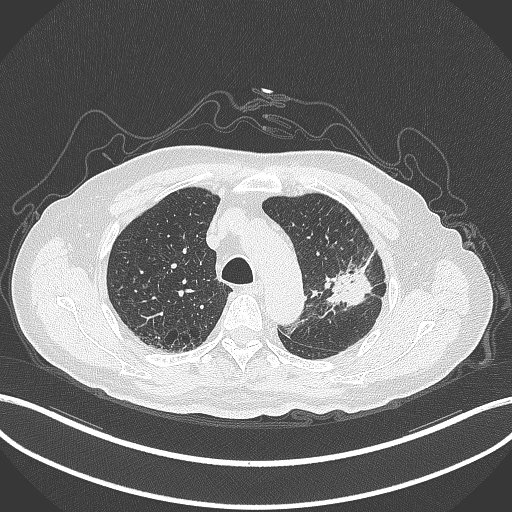
Chest CT, one axial slice. Slice 223 of 331 in the series (ordered by position). Lung window (W 1500 / L -600 HU). 1 mm slice thickness. 512 × 512 image matrix, field of view 400 × 400 mm. Patient: male, 79 years. Case-level facts recorded for this patient, not image findings: clinical TNM (as recorded): T2a N1 M1; histopathological grade: G3.
Outlined on this slice (bounding box drawn by a radiologist):
- lung tumour (recorded histology: adenocarcinoma): box from (x=326, y=250) to (x=383, y=311) px